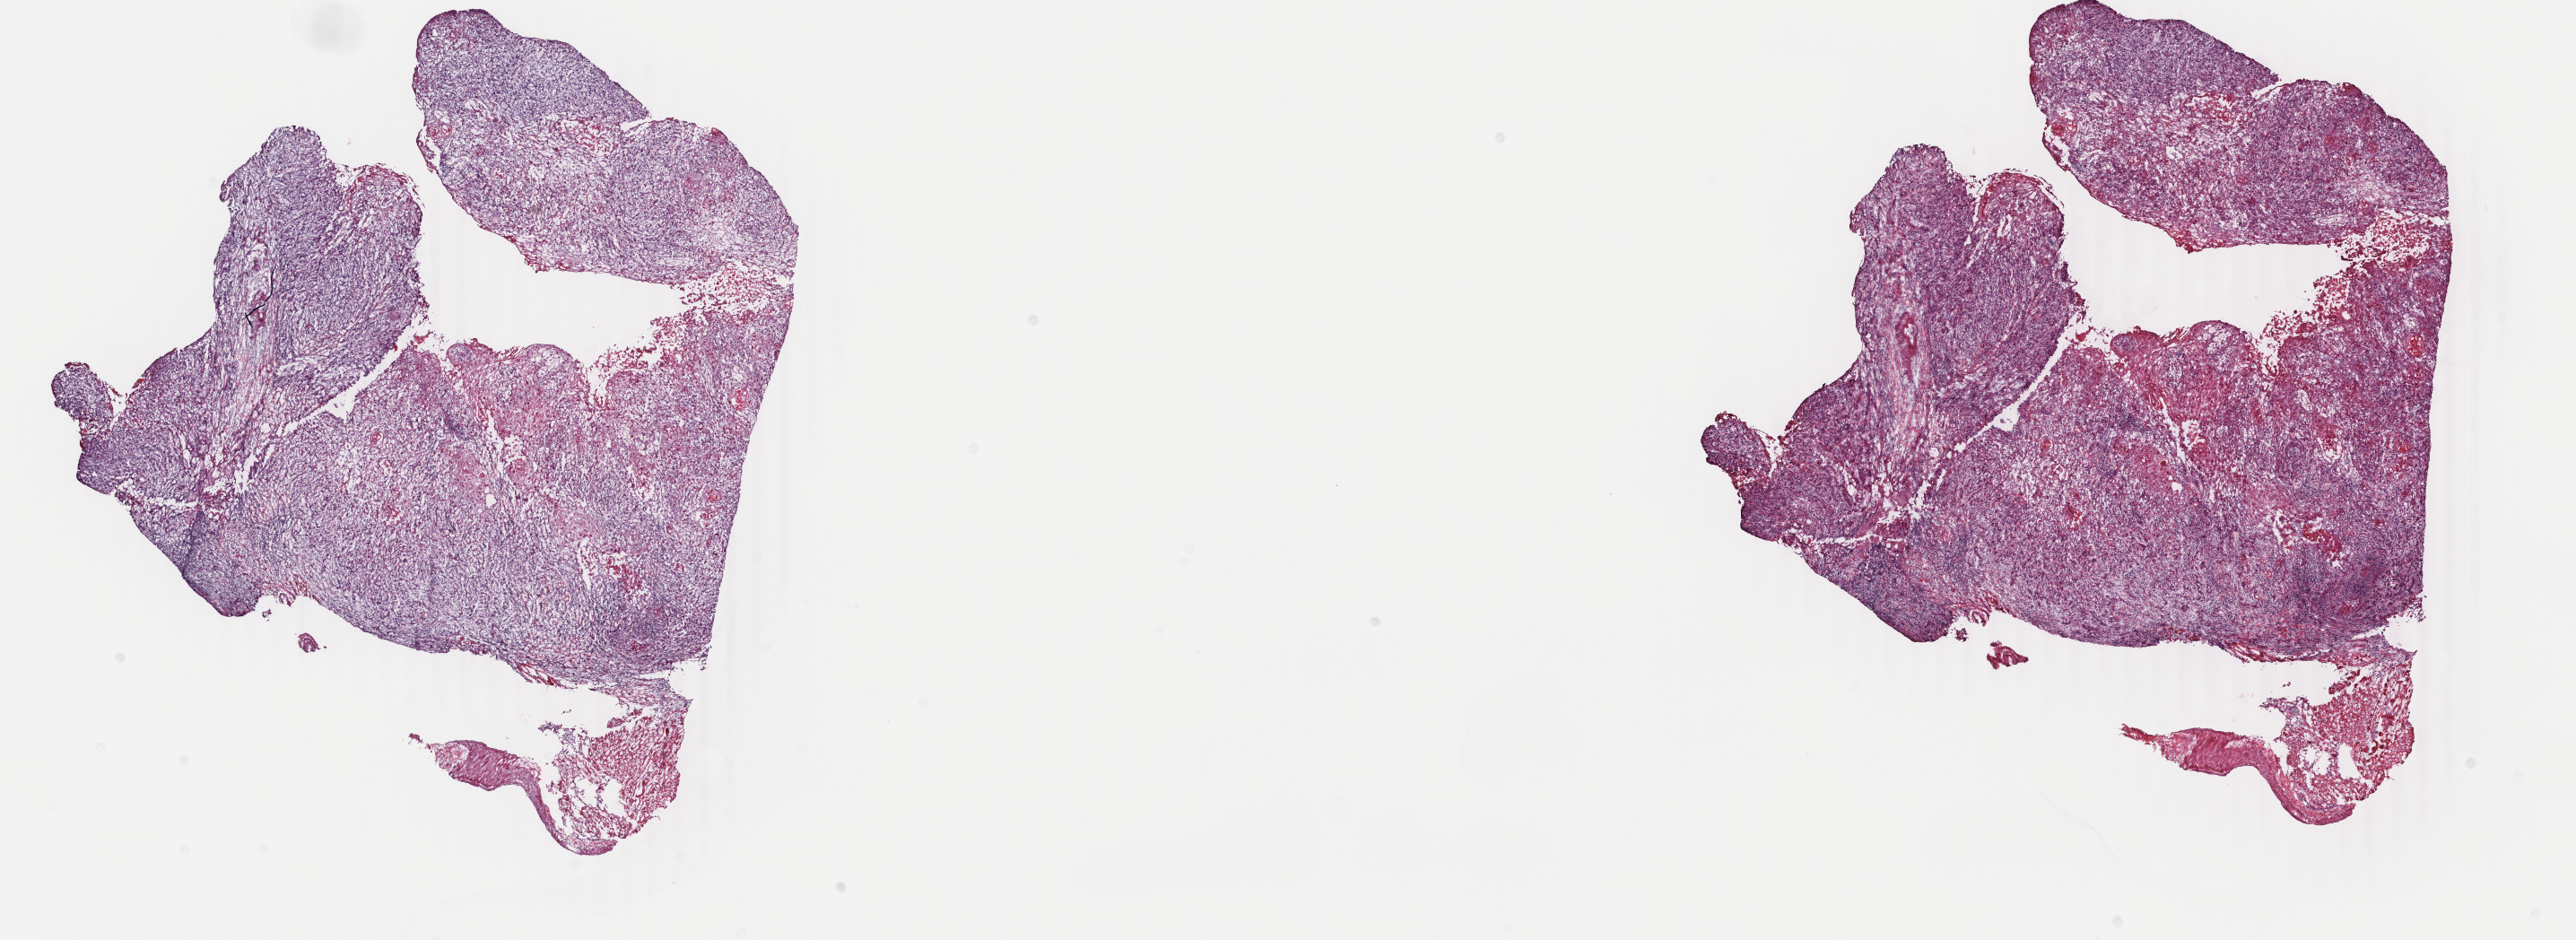
Whole-slide histology image, H&E-stained — shown as a low-resolution overview of the whole scanned area (about 22.8 x 8.3 mm, slide scanned at 40x). Frozen section from the top of the tissue portion. Primary tumour sample from the head and neck. Female, age 40 years at initial diagnosis. Histologic grade: G2 (moderately differentiated). Slide review estimates, as recorded: tumour cells 70%, tumour nuclei 80%, normal cells 0%, stromal cells 30%, necrosis 0%. Inflammatory infiltration, as recorded: lymphocyte infiltration 0%, monocyte infiltration 0%, neutrophil infiltration 0%.
AJCC pathologic stage: IVA (7th edition). Diagnosis: Squamous cell carcinoma, NOS (tongue, NOS).